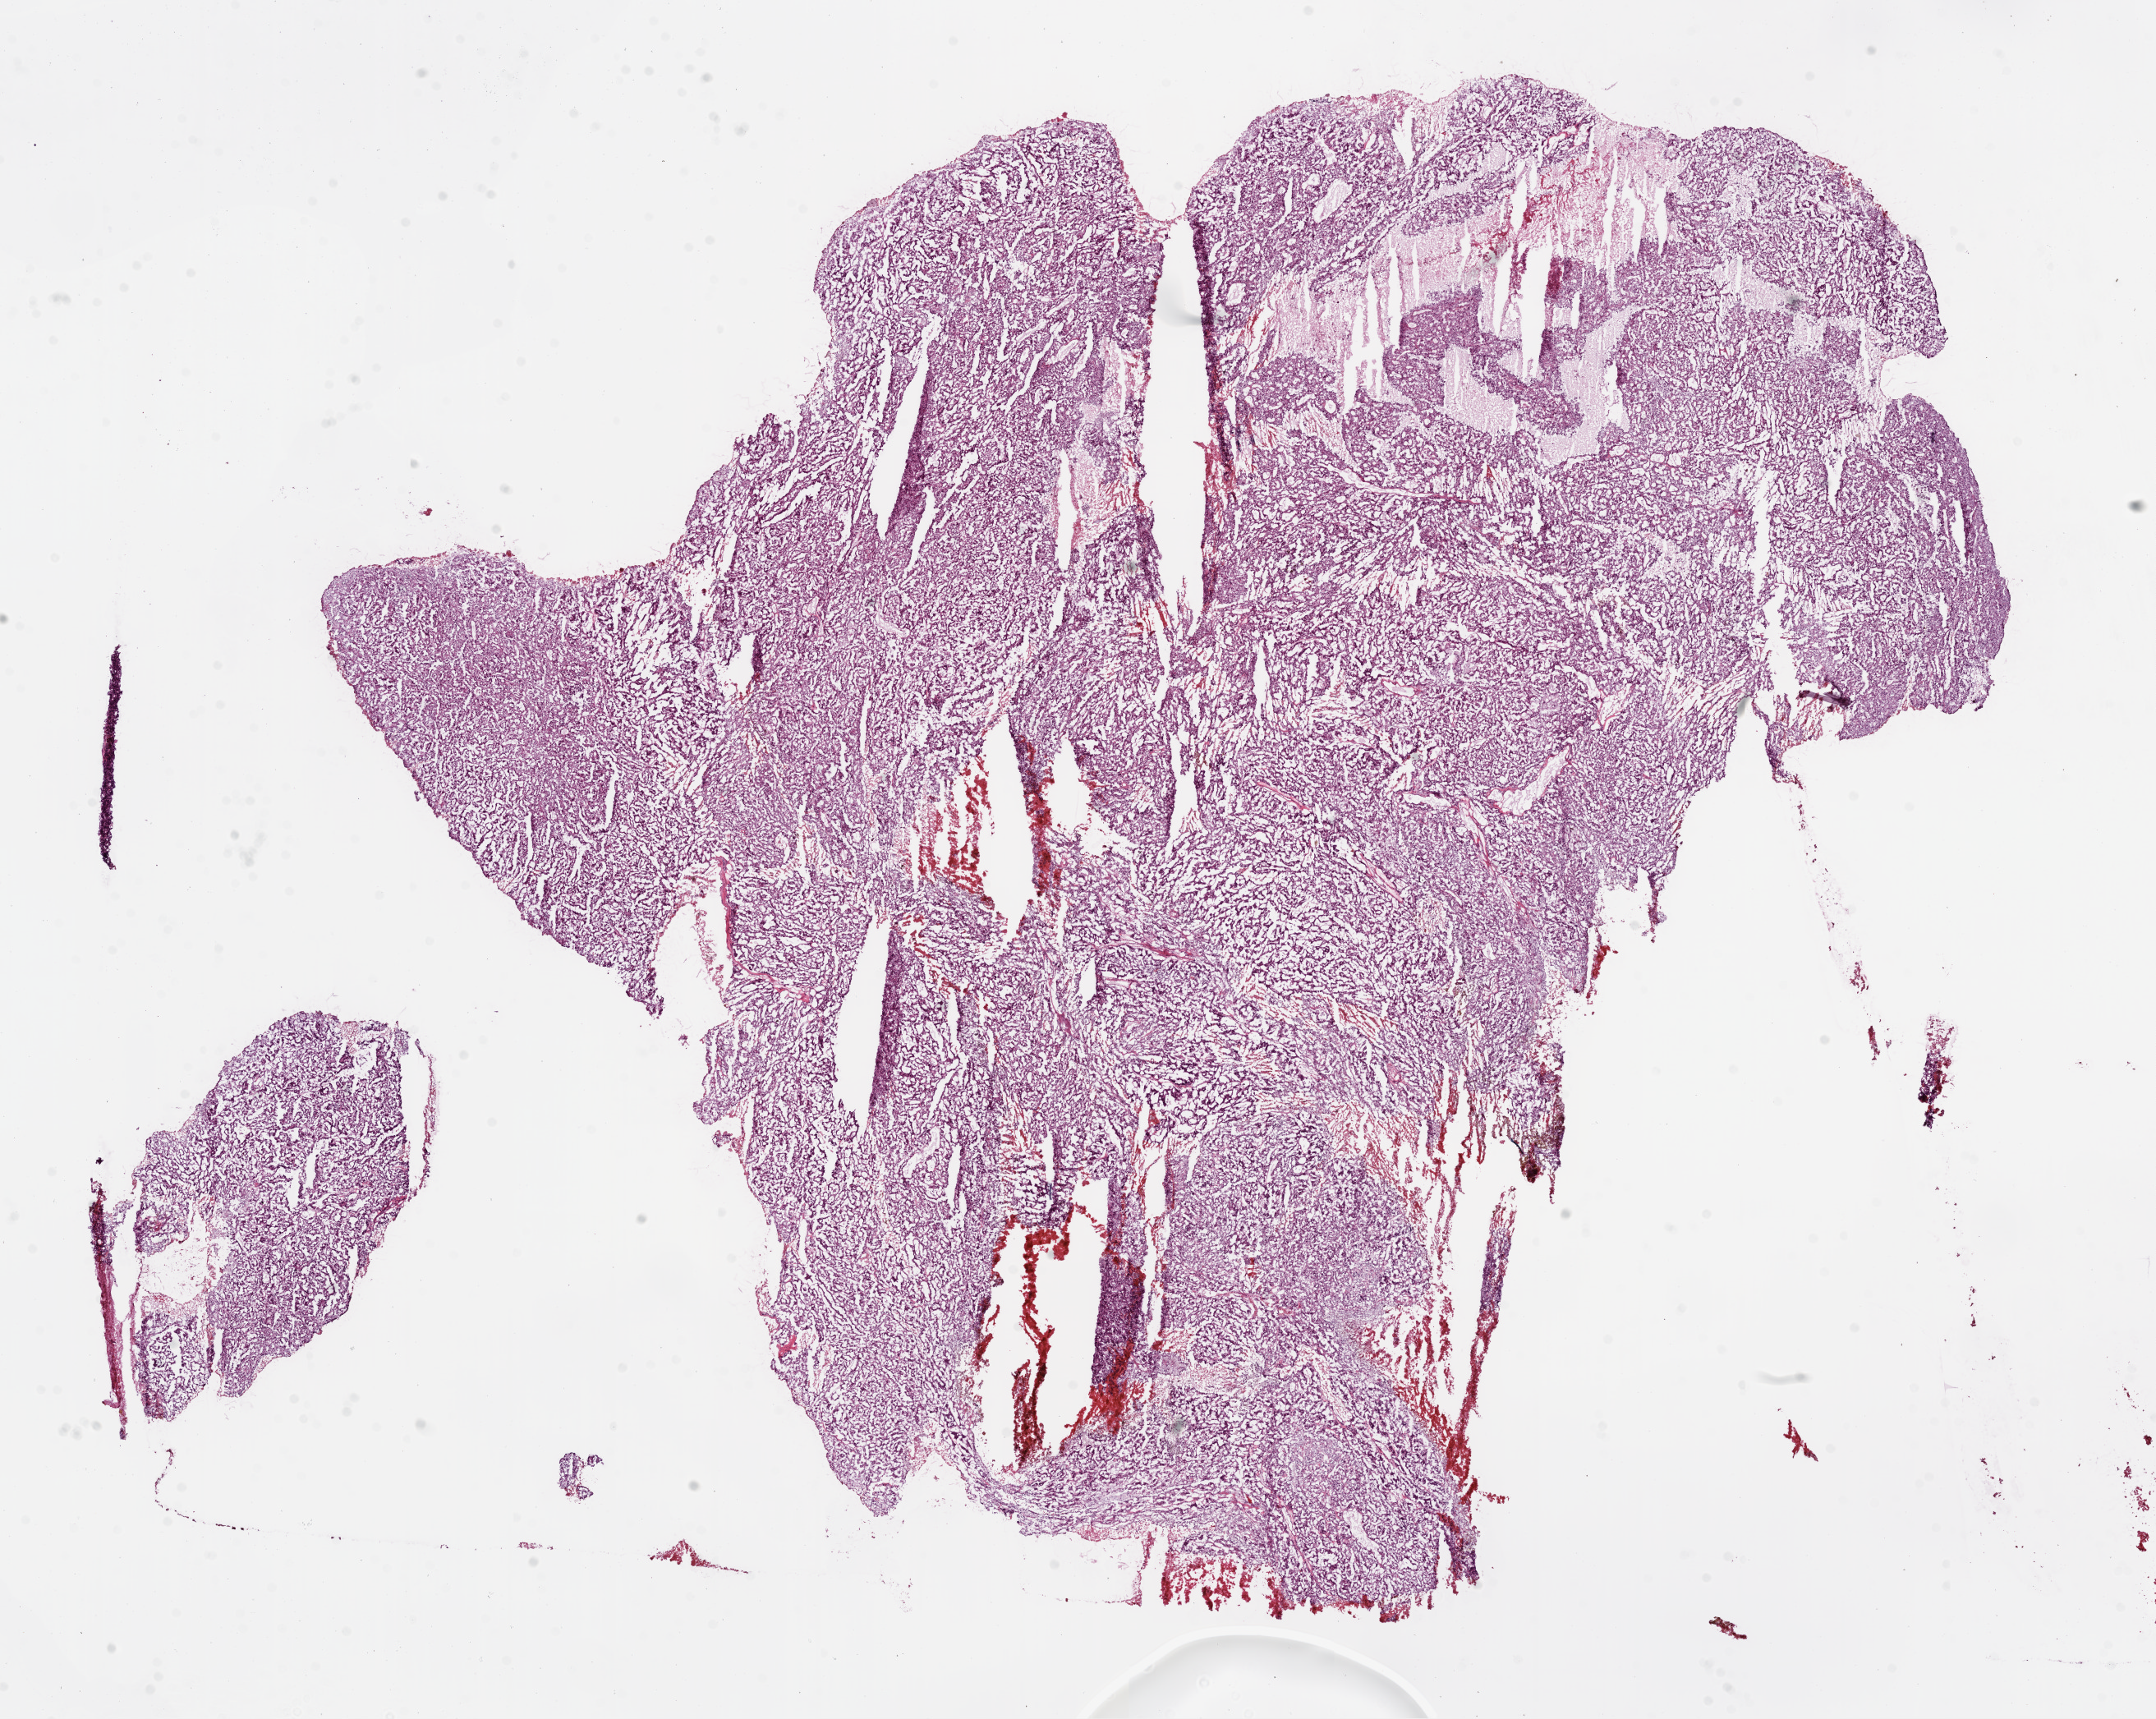
Whole-slide histology image, Hematoxylin and eosin (H&E) stained — low-resolution overview of the scanned area, about 21.1 x 16.8 mm. Frozen section from the bottom of the tissue portion. Kidney, primary tumour sample. Patient: female, age at initial diagnosis 62 years. Histologic grade: G2 (moderately differentiated). Composition of this section per pathologist review: tumour cells 90%, tumour nuclei 90%, normal cells 0%, stromal cells 0%, necrosis 10%. Inflammatory infiltration, as recorded: lymphocyte infiltration 2%.
Histologic diagnosis: Clear cell adenocarcinoma, NOS. Laterality: right. AJCC pathologic stage: I.